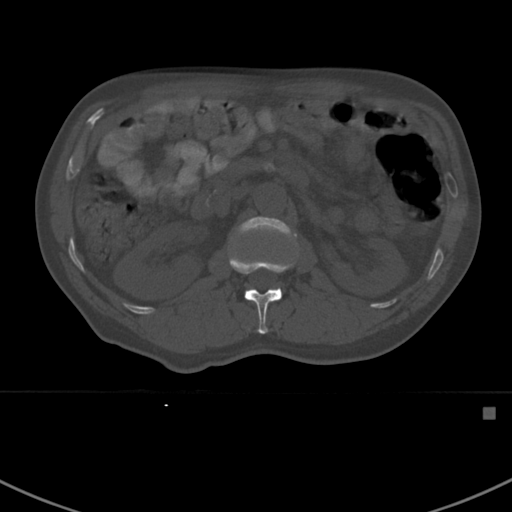
CT including the spine, one axial slice. Position 302 of 412 along the scan axis. Reconstruction kernel Br40s. Bone window (W 1800 / L 400 HU). 512 × 512 image matrix, field of view 358 × 358 mm. Male patient, age 59 years. Case-level facts recorded for this patient, not image findings: primary cancer: prostate.
Annotated regions visible in this slice (semi-automatically segmented with operator editing):
- L1 vertebra: box from (x=230, y=251) to (x=293, y=334) px
- L2 vertebra: (x=232, y=216)–(x=297, y=245)